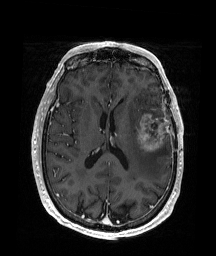
Brain MRI from a brain-tumour surgery series, one axial slice; position 84 of 176 along the scan axis; T1-weighted post-contrast; 1 mm slice thickness; 216 × 256 image matrix, field of view 219 × 260 mm. Case-level facts recorded for this patient, not image findings: histopathology: Glioblastoma; WHO grade: 4; IDH mutation: no; tumour location: Left Frontal.
Structures marked on this image (outlined manually by an expert reader):
- tumour: bounding box <135,113,169,152> (left, top, right, bottom; pixels)